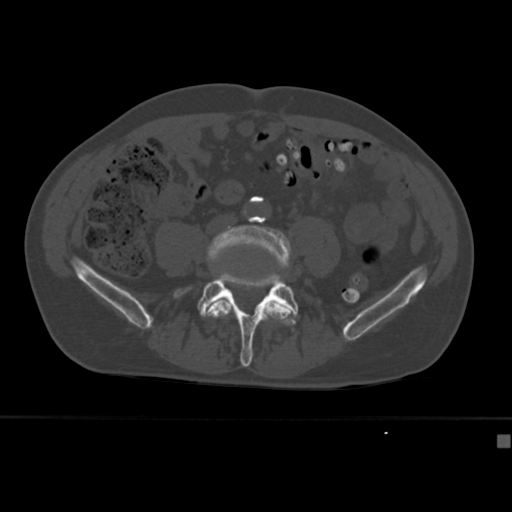
CT including the spine, one axial slice. Slice 94 of 430 in the series (ordered by position). 120 kVp. Bone window (W 1800 / L 400 HU). 1.5 mm slice thickness. 512 × 512 image matrix. Male patient, age 64 years. From the clinical record (not read from this slice): primary cancer: uterus; vertebrae with lytic lesions (as recorded): T1, T4, T5, T7, L5.
Outlined on this slice (semi-automatically segmented with operator editing):
- L4 vertebra: bounding box <205,225,292,323> (left, top, right, bottom; pixels)
- L5 vertebra: <174,272,299,367>